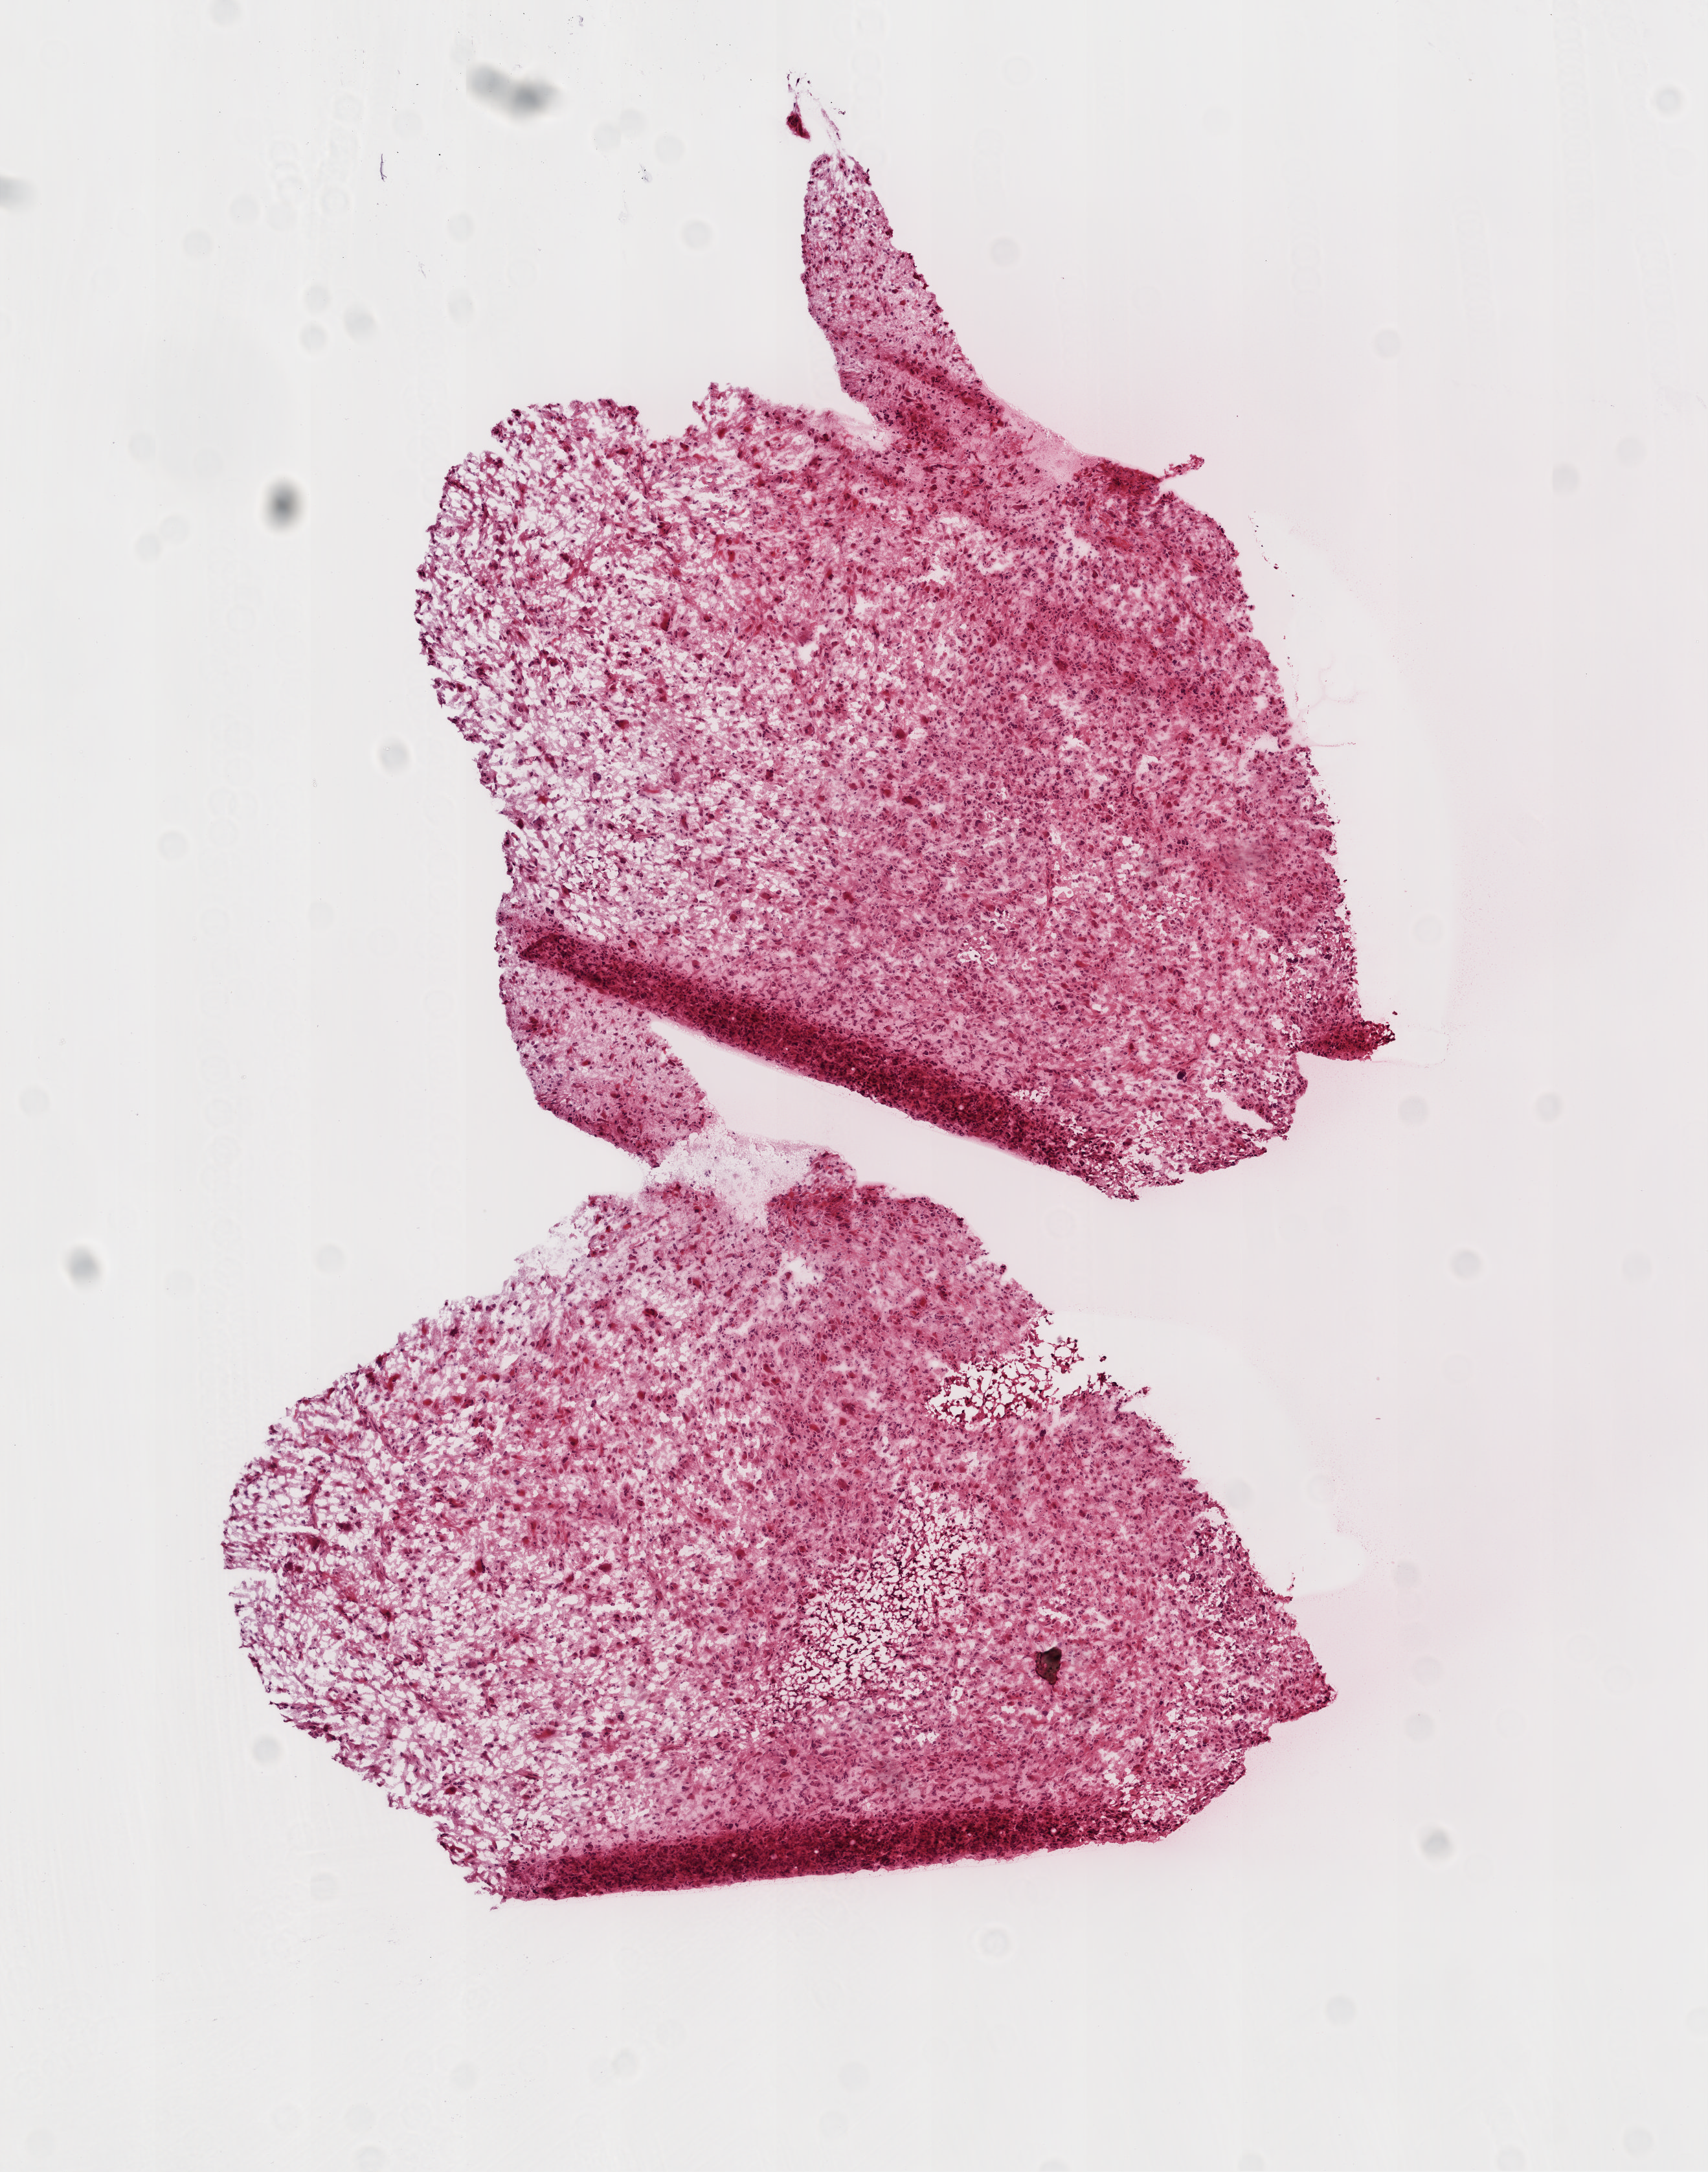
Hematoxylin and eosin (H&E) stained whole-slide image, shown as a low-resolution overview of the whole scanned area (about 5.3 x 6.8 mm, from a 20x scan). Frozen section from the top of the tissue portion. Sample: primary tumour, brain. Patient: male, age at initial diagnosis 57 years. Slide review estimates, as recorded: tumour cells 95%, tumour nuclei 95%, stromal cells 5%, necrosis 0%.
Histologic diagnosis: Glioblastoma.